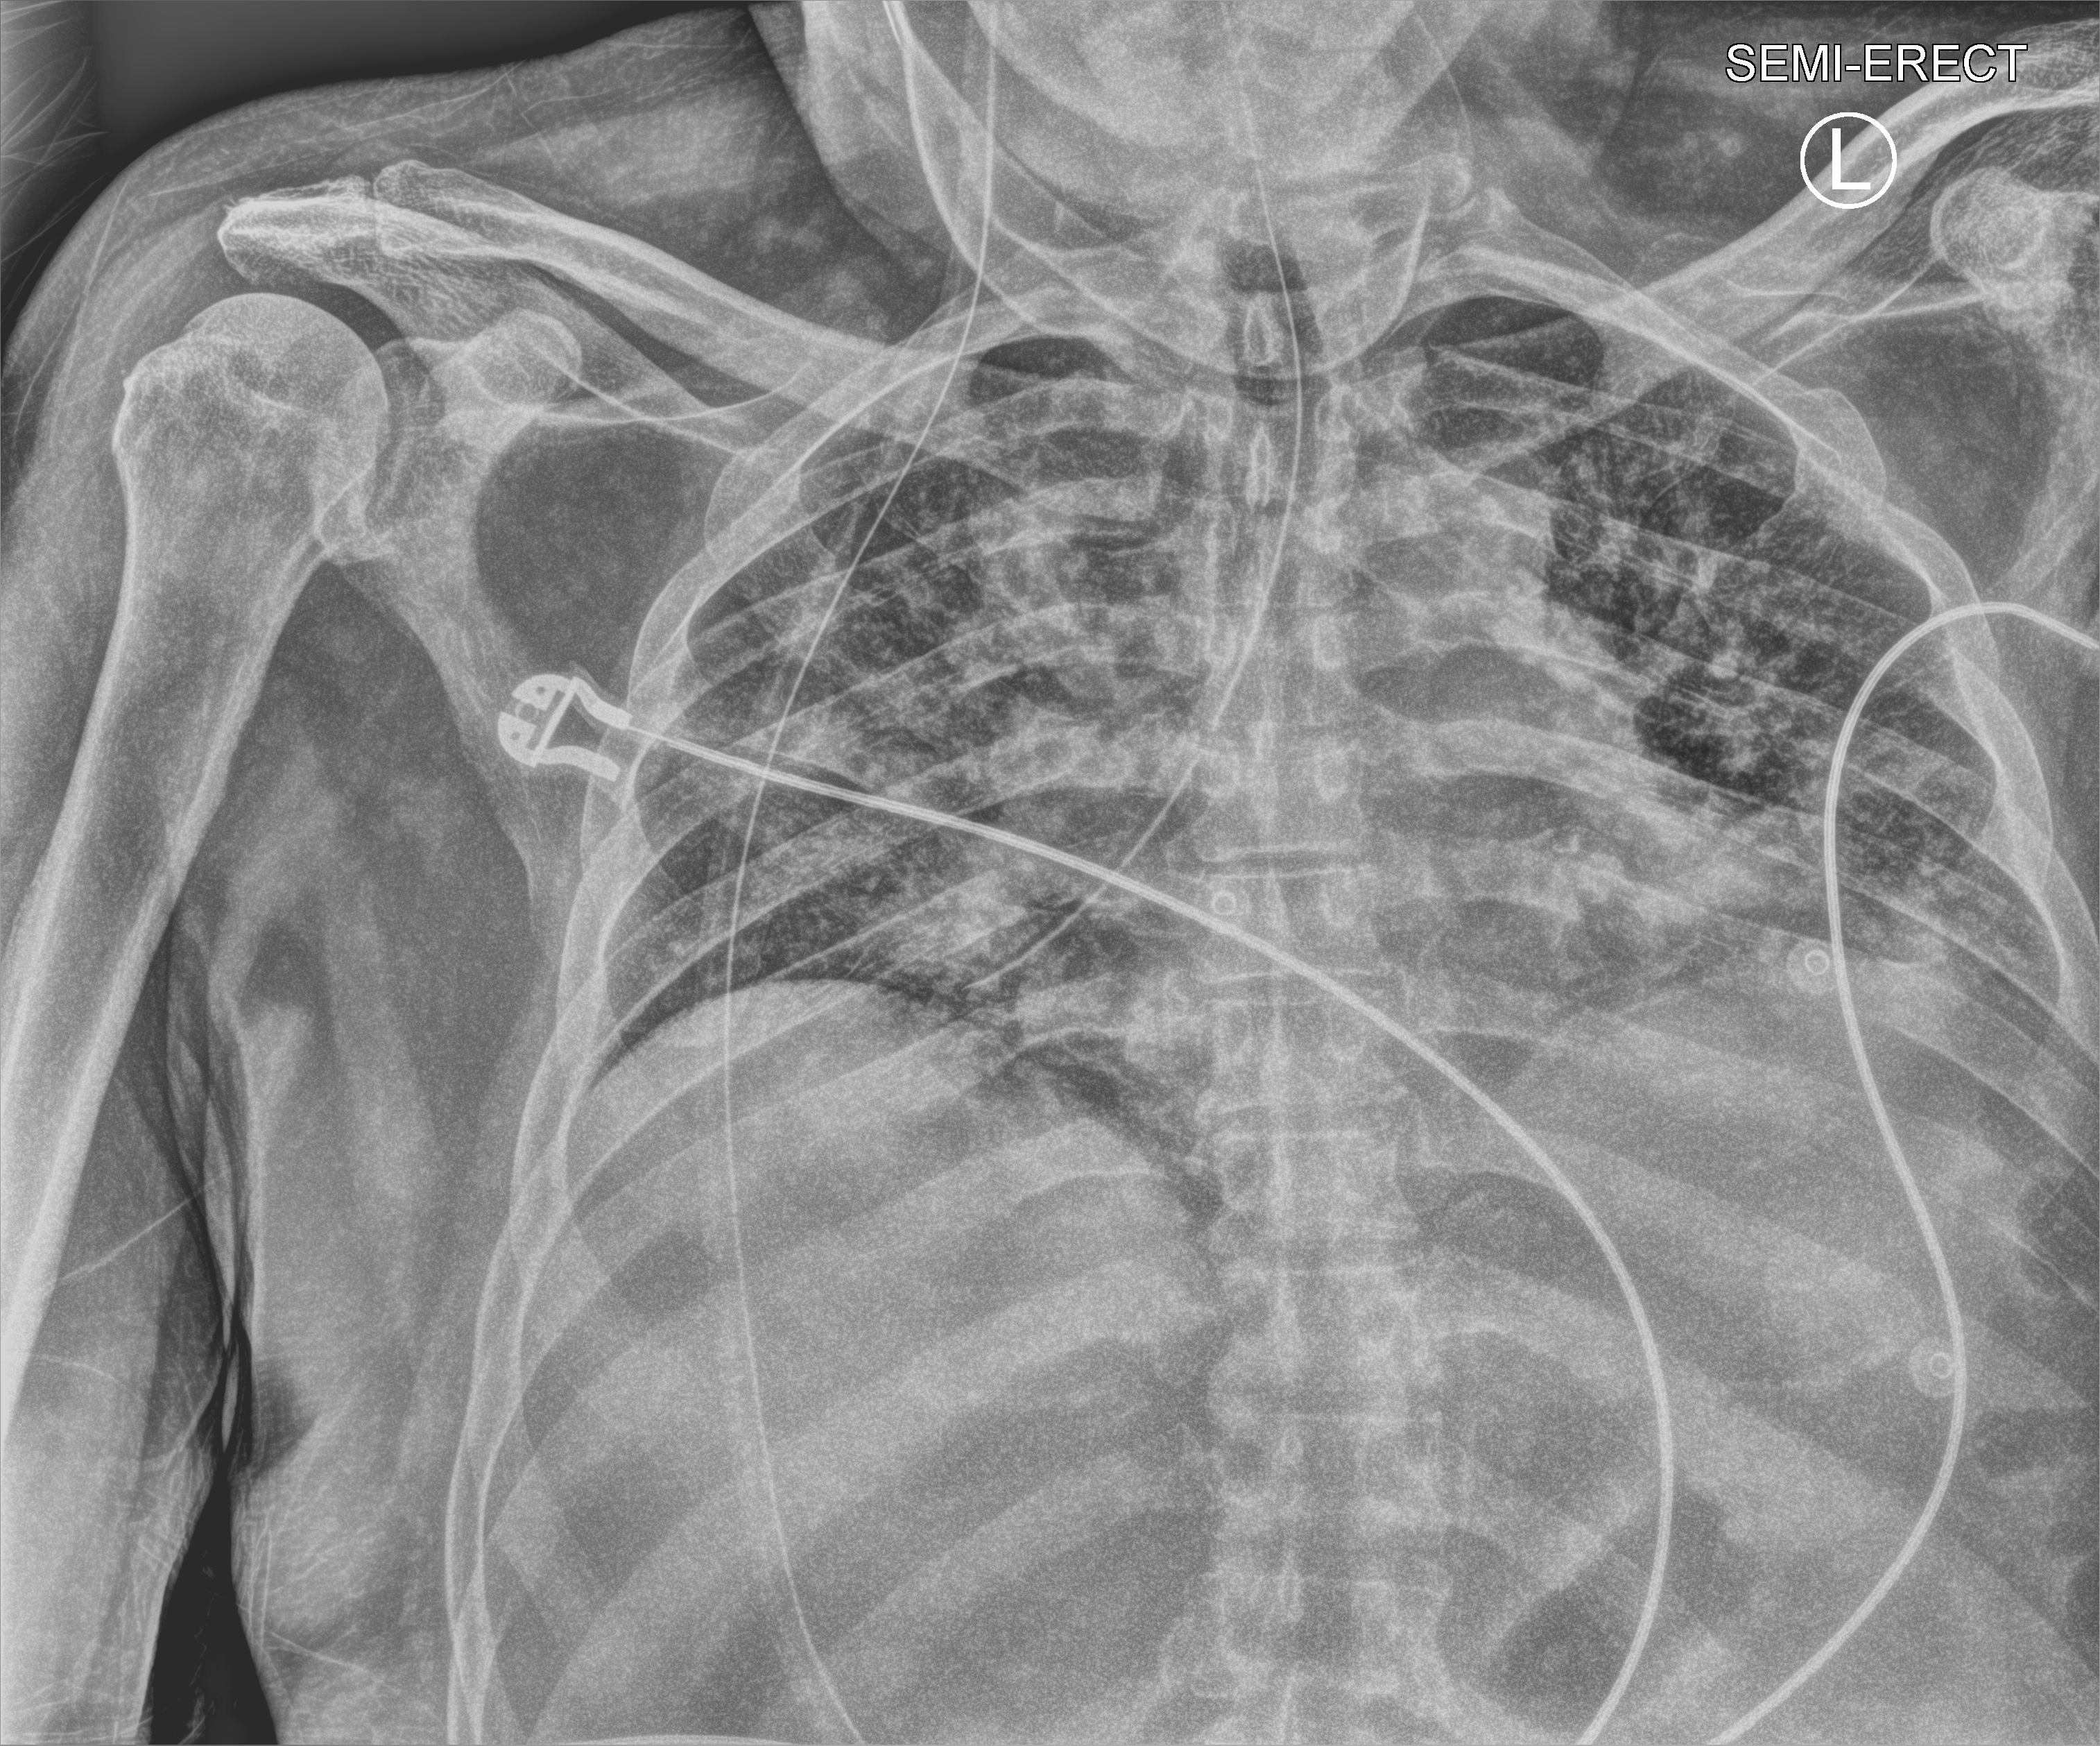
Chest X-ray (portable); anteroposterior (AP) projection. Patient hospitalised with COVID-19; male, aged 60–74 years.
Hospital-stay facts (about this admission, not read from this image; timing relative to this image not recorded): admitted to intensive care during this hospital stay: no; mechanically ventilated during this hospital stay: no; hypertension (admission record): yes.